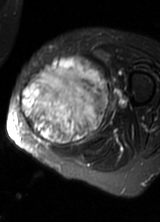
MRI of an extremity soft-tissue mass, one axial slice; slice 28 of 69 in the series (ordered by position); T2-weighted fat-saturated; MR volume resampled by the dataset authors to the PET/CT grid (not the native acquisition matrix); 3.27 mm slice thickness; 160 × 222 image matrix, field of view 156 × 217 mm. Female patient. From the clinical record (not read from this slice): histological type: pleomorphic leiomyosarcoma; grade: high; site of the primary tumour: left thigh.
Outlined on this slice (expert contour drawn on MRI and transferred to this co-registered scan by the dataset authors):
- gross tumour volume including surrounding oedema: box from (x=20, y=57) to (x=110, y=149) px
- gross tumour volume (mass): (x=20, y=57)–(x=108, y=146)